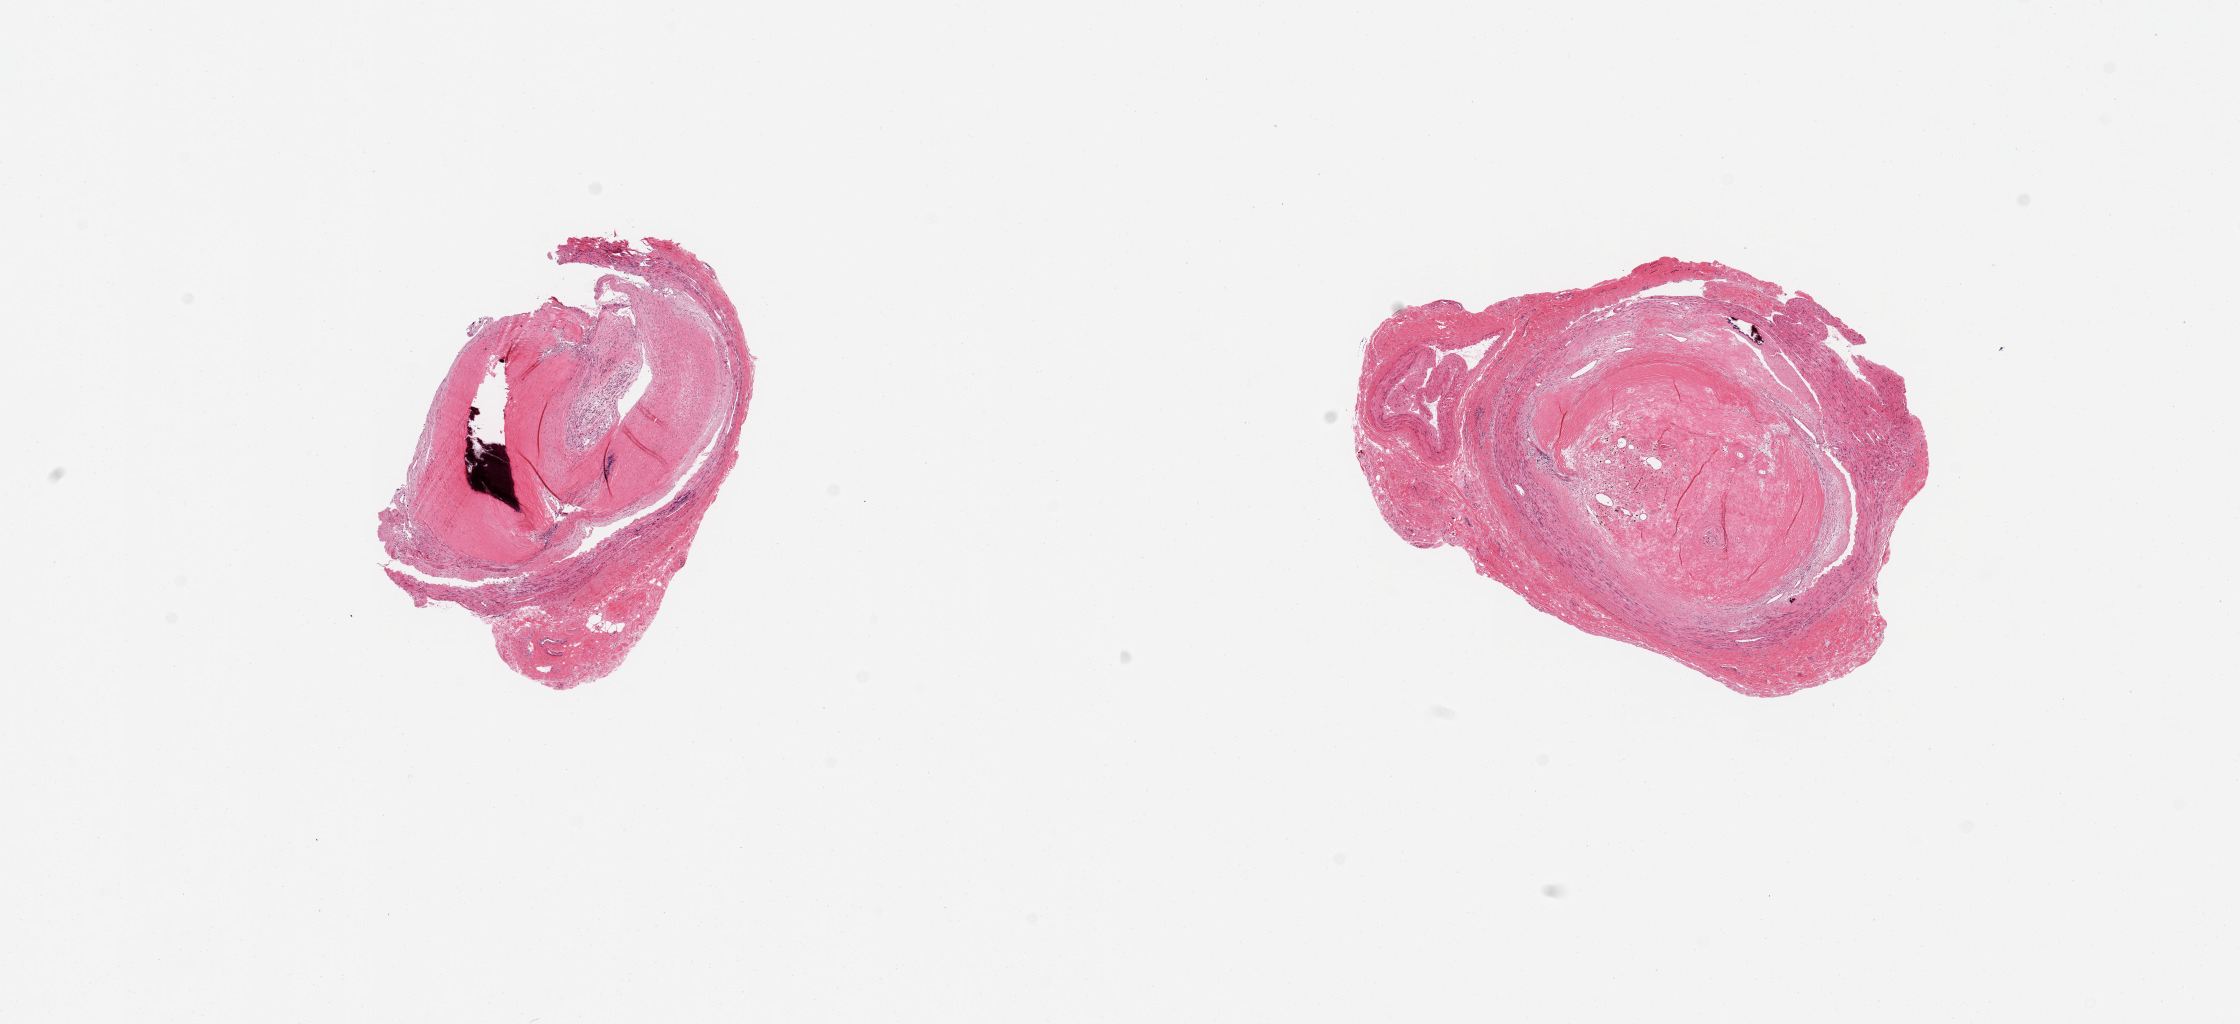
Hematoxylin and eosin (H&E) whole-slide image — low-resolution overview of the scanned area, about 17.7 x 8.1 mm (acquisition: 20x scan); PAXgene-fixed, paraffin-embedded tissue; sampled site (target tissue): tibial artery; donor tissue sample. Donor: male.
- pathologist's review note for this sample: 2 pieces, occlusive atherosis, focally calcified